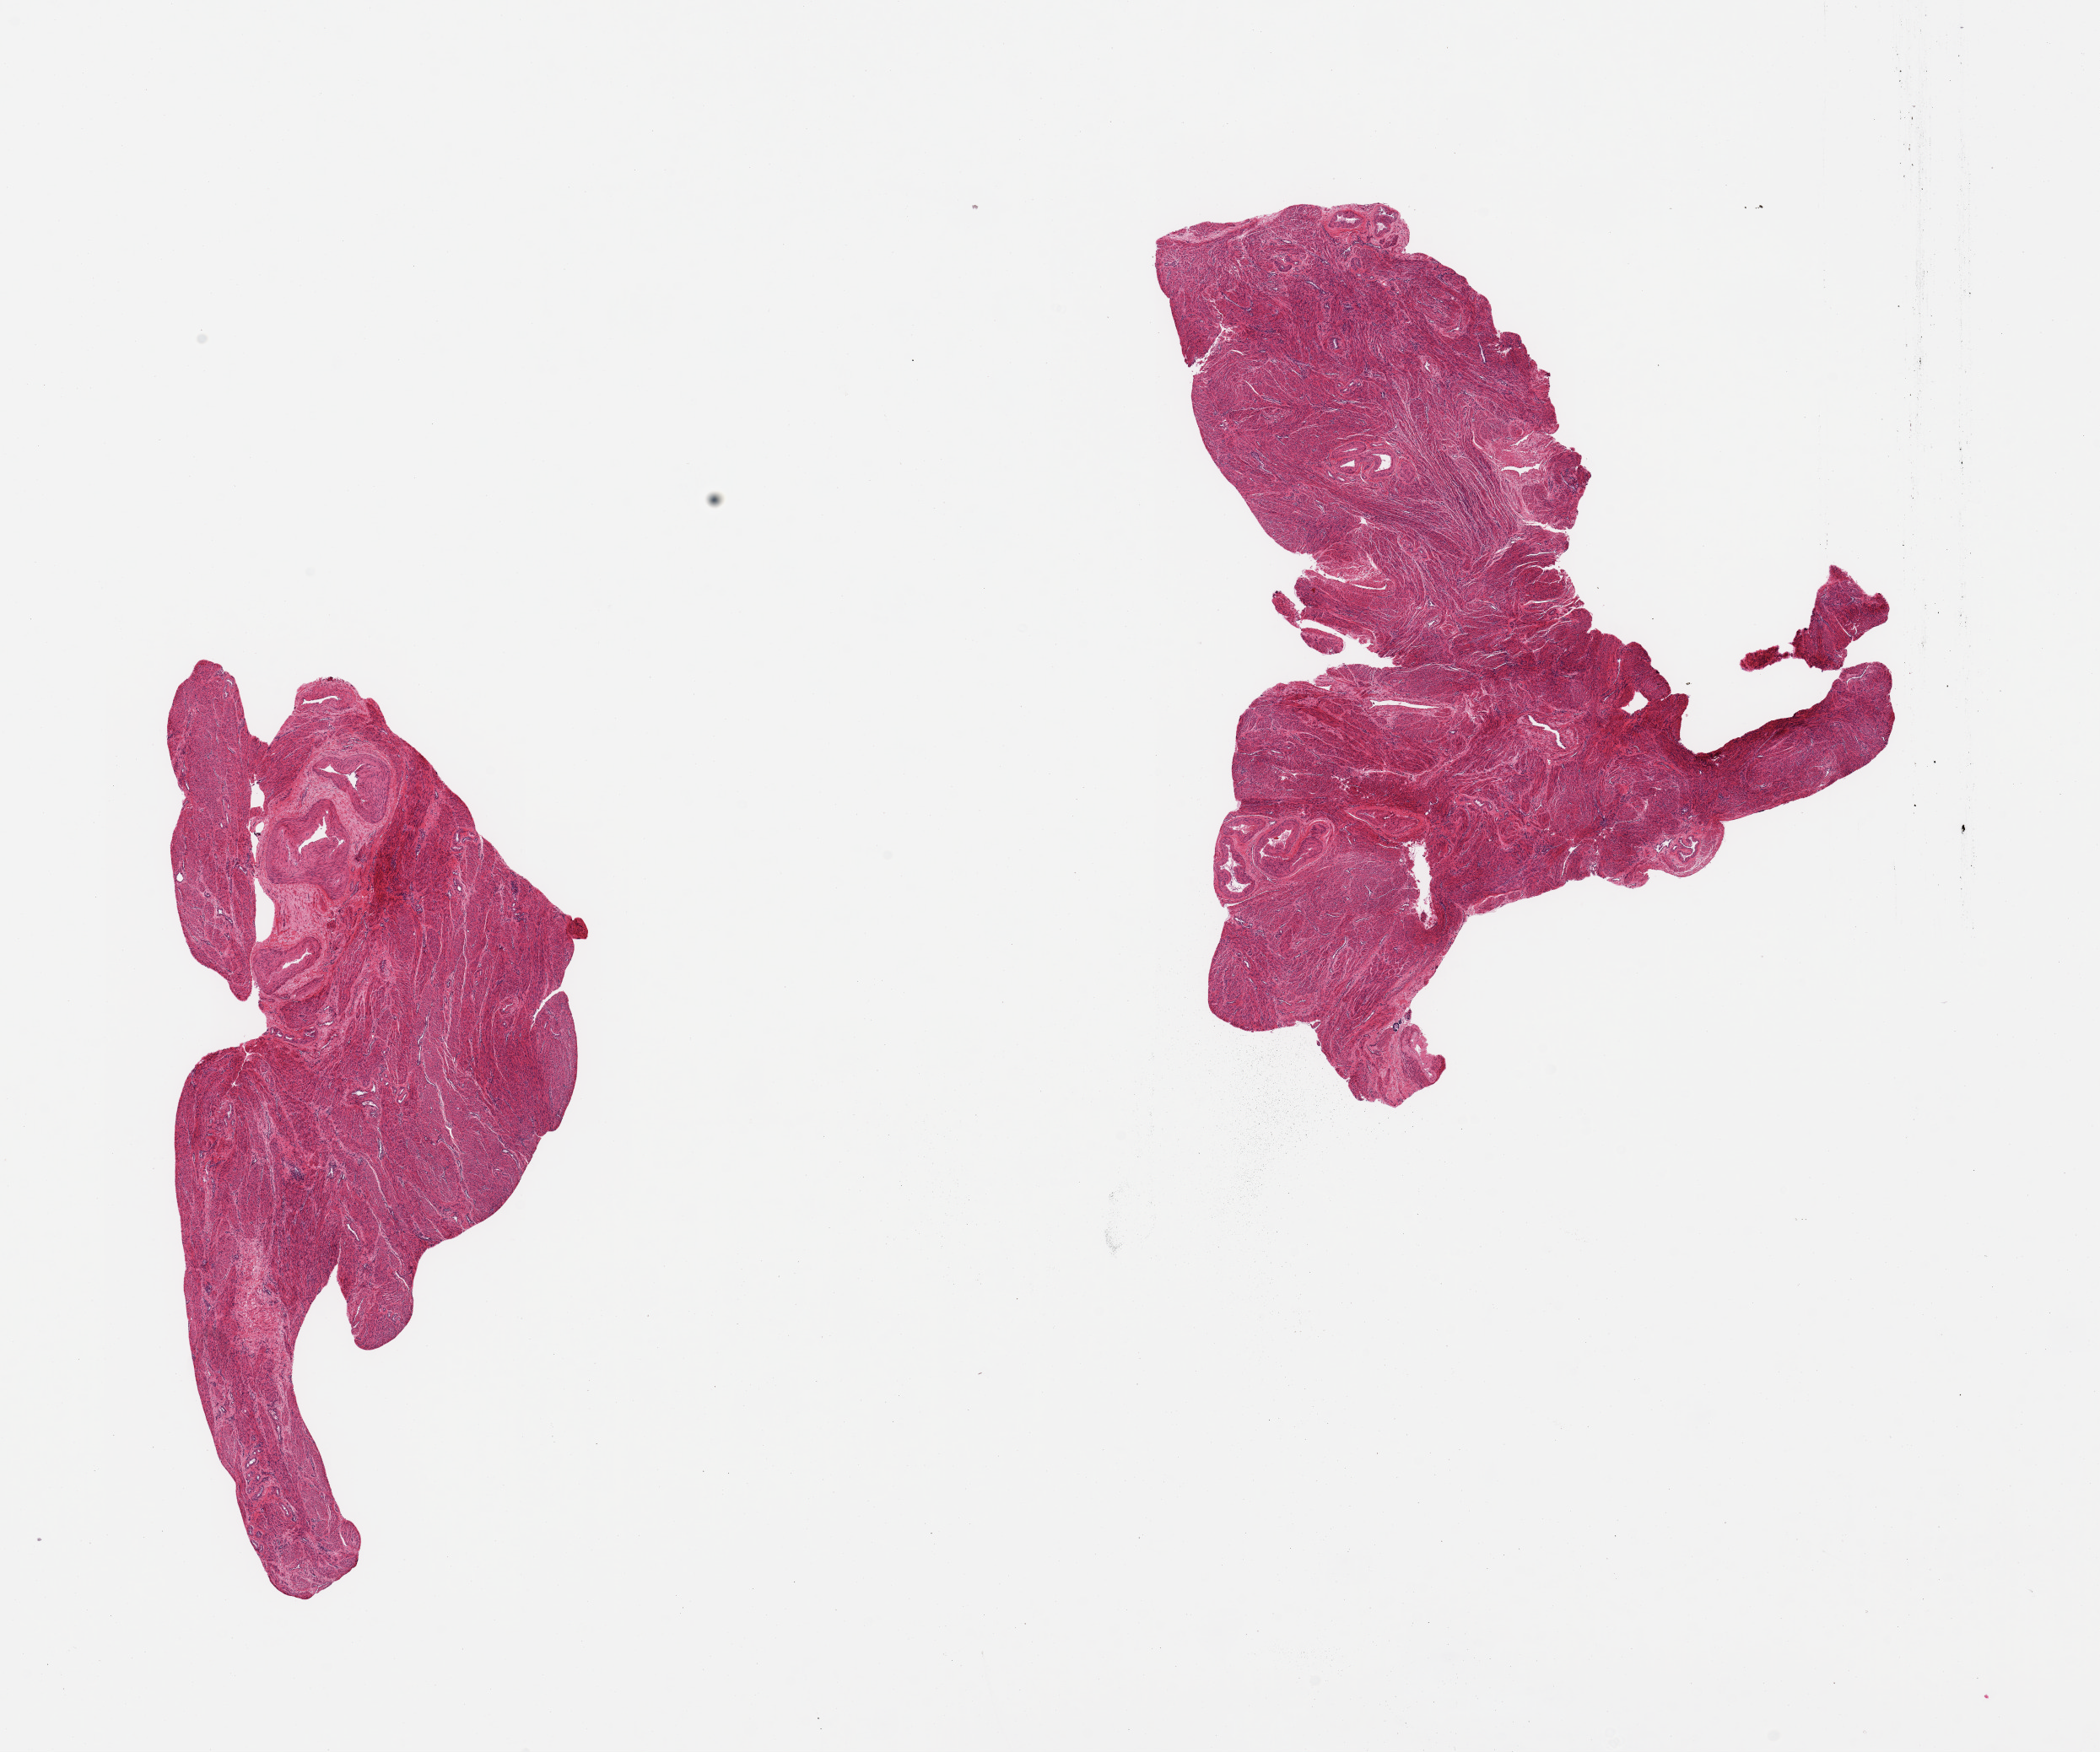
Digitized hematoxylin and eosin (H&E)-stained section — whole scanned area (about 19.7 x 16.4 mm) shown as a low-resolution overview. PAXgene-fixed, paraffin-embedded tissue. Target tissue: uterus. Donor tissue sample. Donor sex: female.
* review note (as recorded): 2 pieces; myometrium